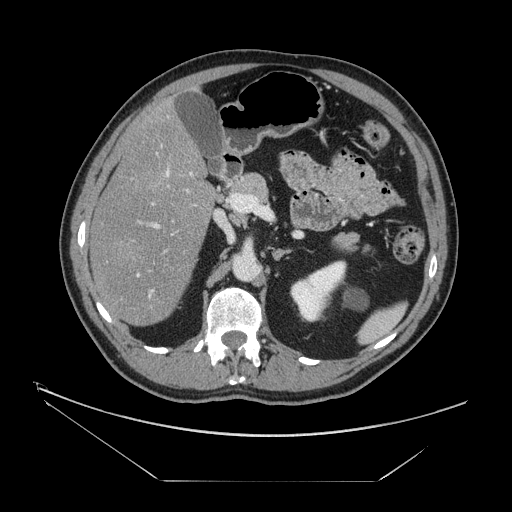
Contrast-enhanced abdominal CT, one axial slice. Position 79 of 161 along the scan axis. Reconstruction kernel STANDARD. 120 kVp. Intravenous contrast given. Soft-tissue window (W 400 / L 40 HU). 2.5 mm slice thickness. 512 × 512 image matrix, field of view 440 × 440 mm. Male patient, age 65 years. Case-level facts recorded for this patient, not image findings: diagnosis: colorectal cancer liver metastases, imaged before liver resection; multiple liver metastases: yes; largest metastasis: 4.2 cm; disease in both lobes: yes.
Outlined on this slice (expert manual segmentation):
- hepatic veins: bounding box <132,167,174,299> (left, top, right, bottom; pixels)
- liver: <90,101,215,326>
- planned liver remnant (the part of the liver to remain after resection): <109,102,205,325>
- portal vein (with intrahepatic branches): <111,153,203,323>